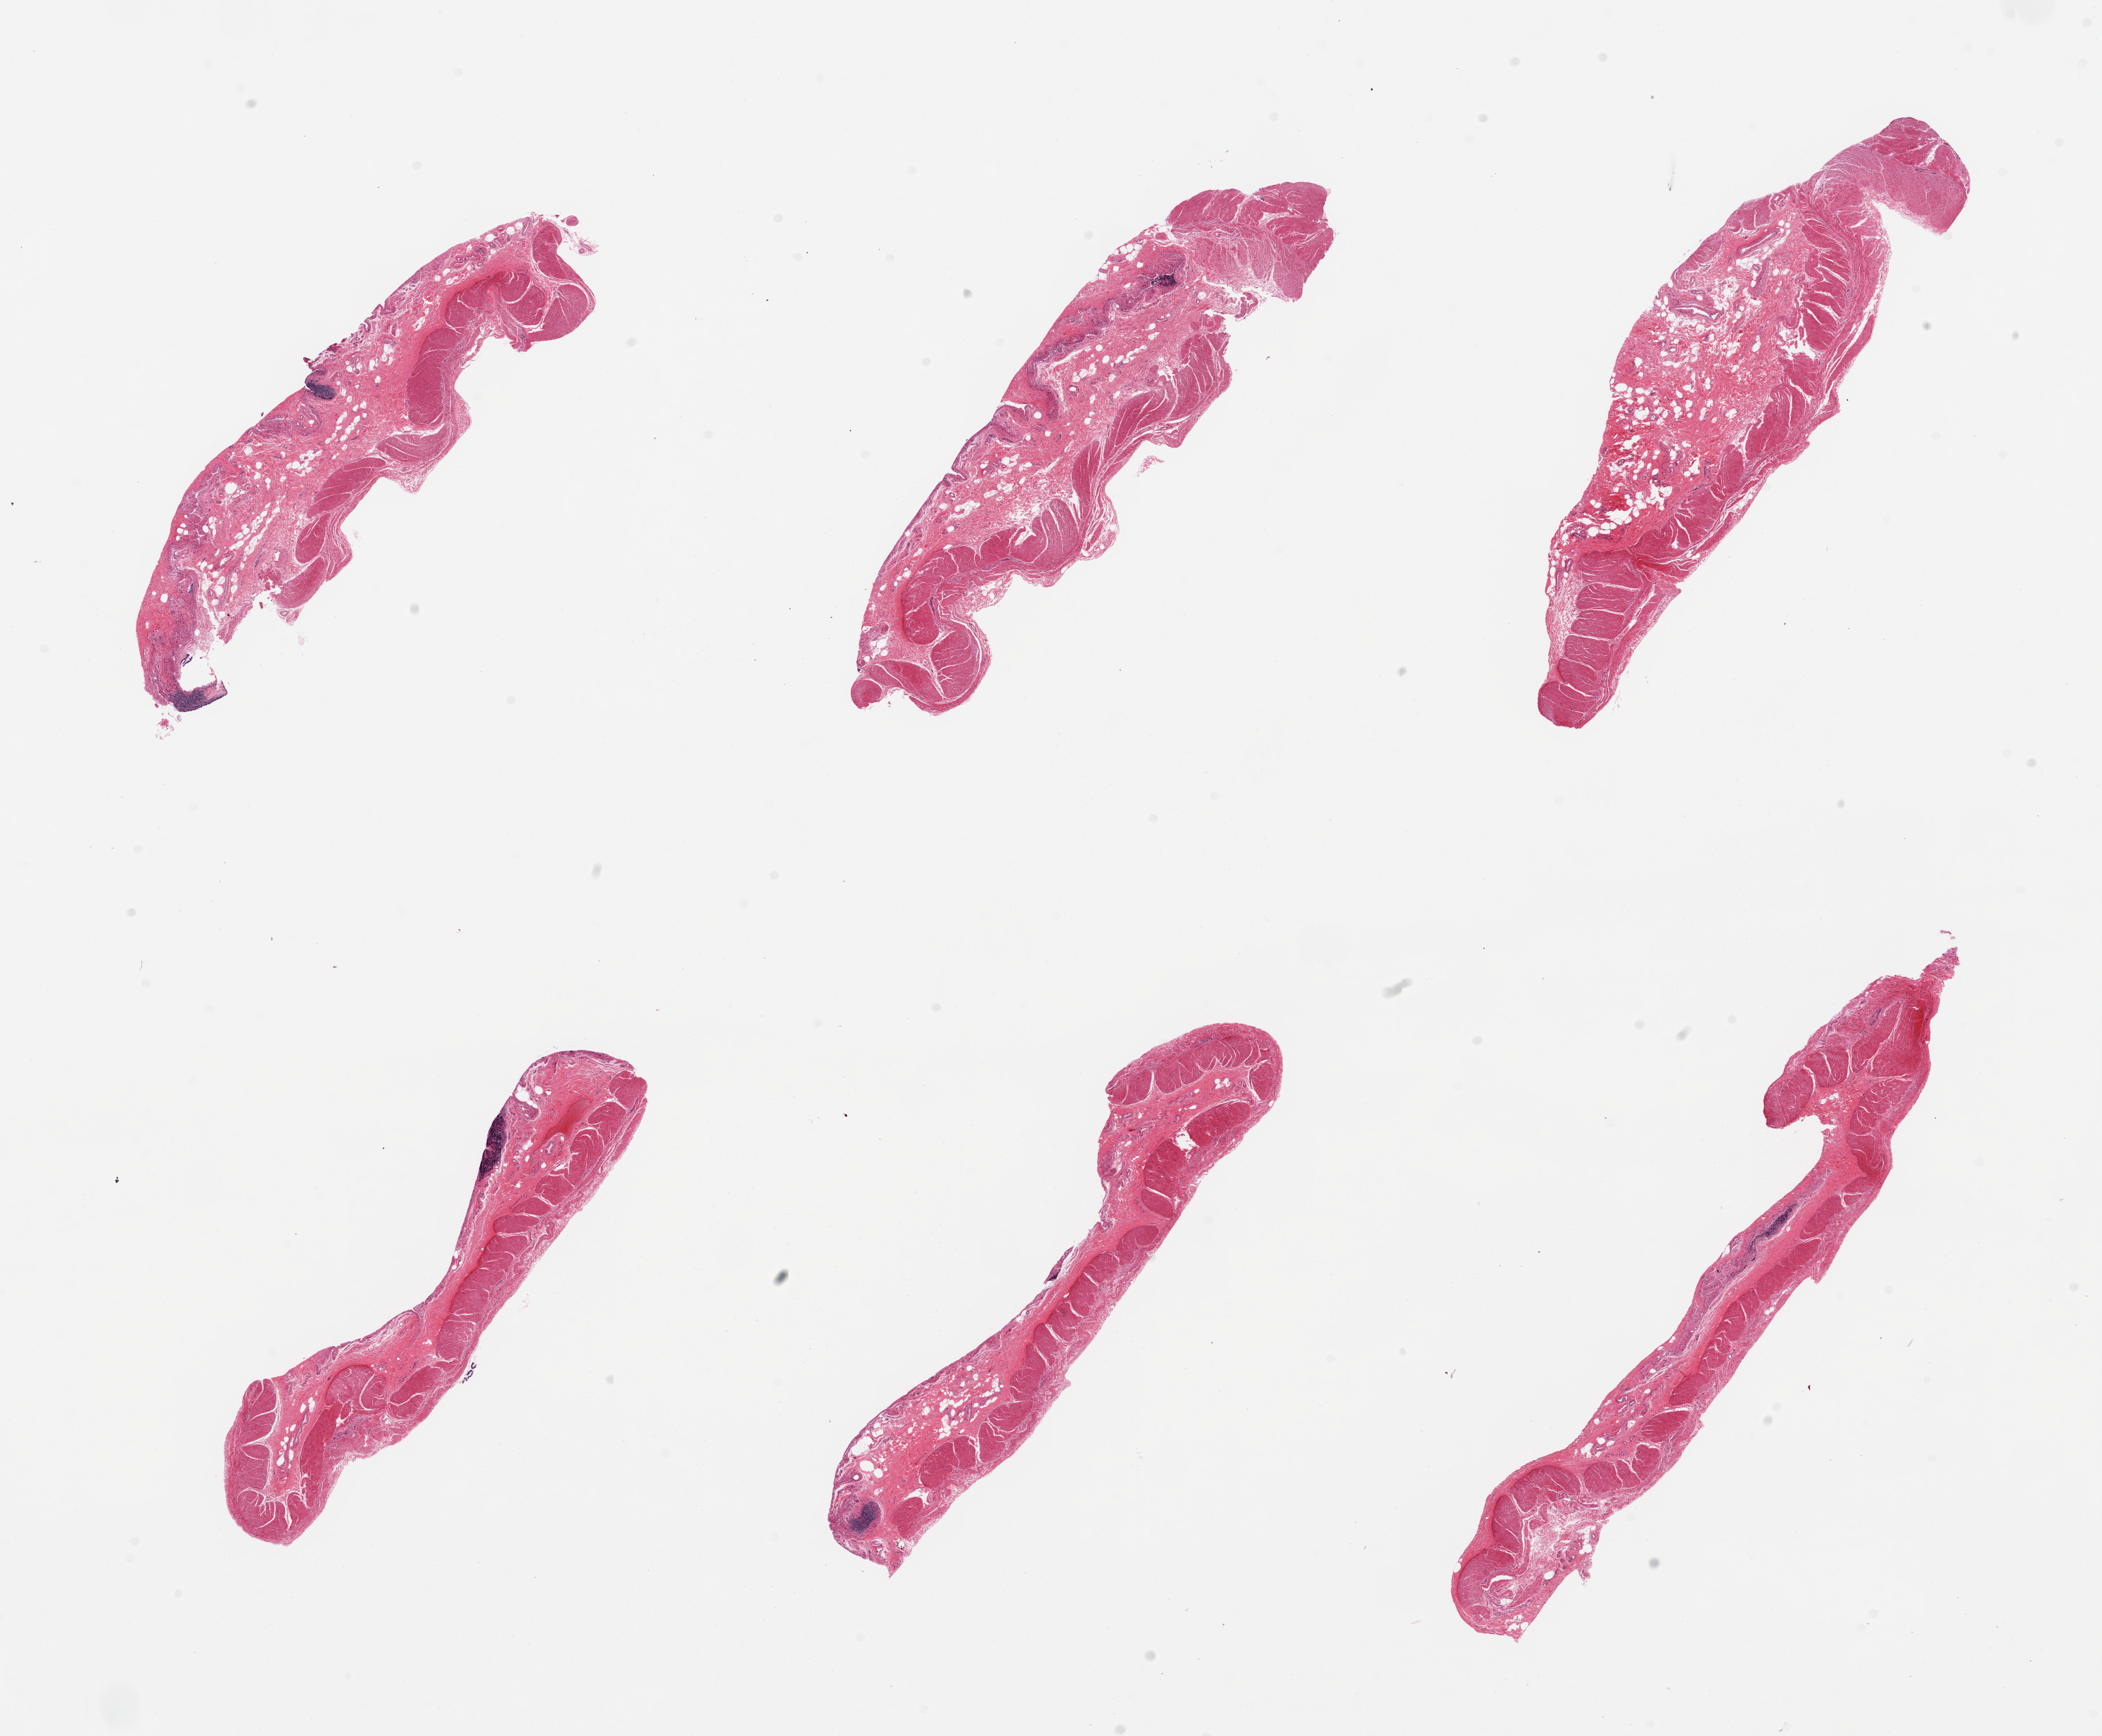
Hematoxylin and eosin (H&E) whole-slide image, brightfield — shown as a low-resolution overview of the whole scanned area (about 23.6 x 19.5 mm), PAXgene-fixed, paraffin-embedded tissue, target tissue: sigmoid colon, donor tissue sample. Donor: male.
Reviewer comment on this tissue sample: 6 pieces, musularis and serosa.